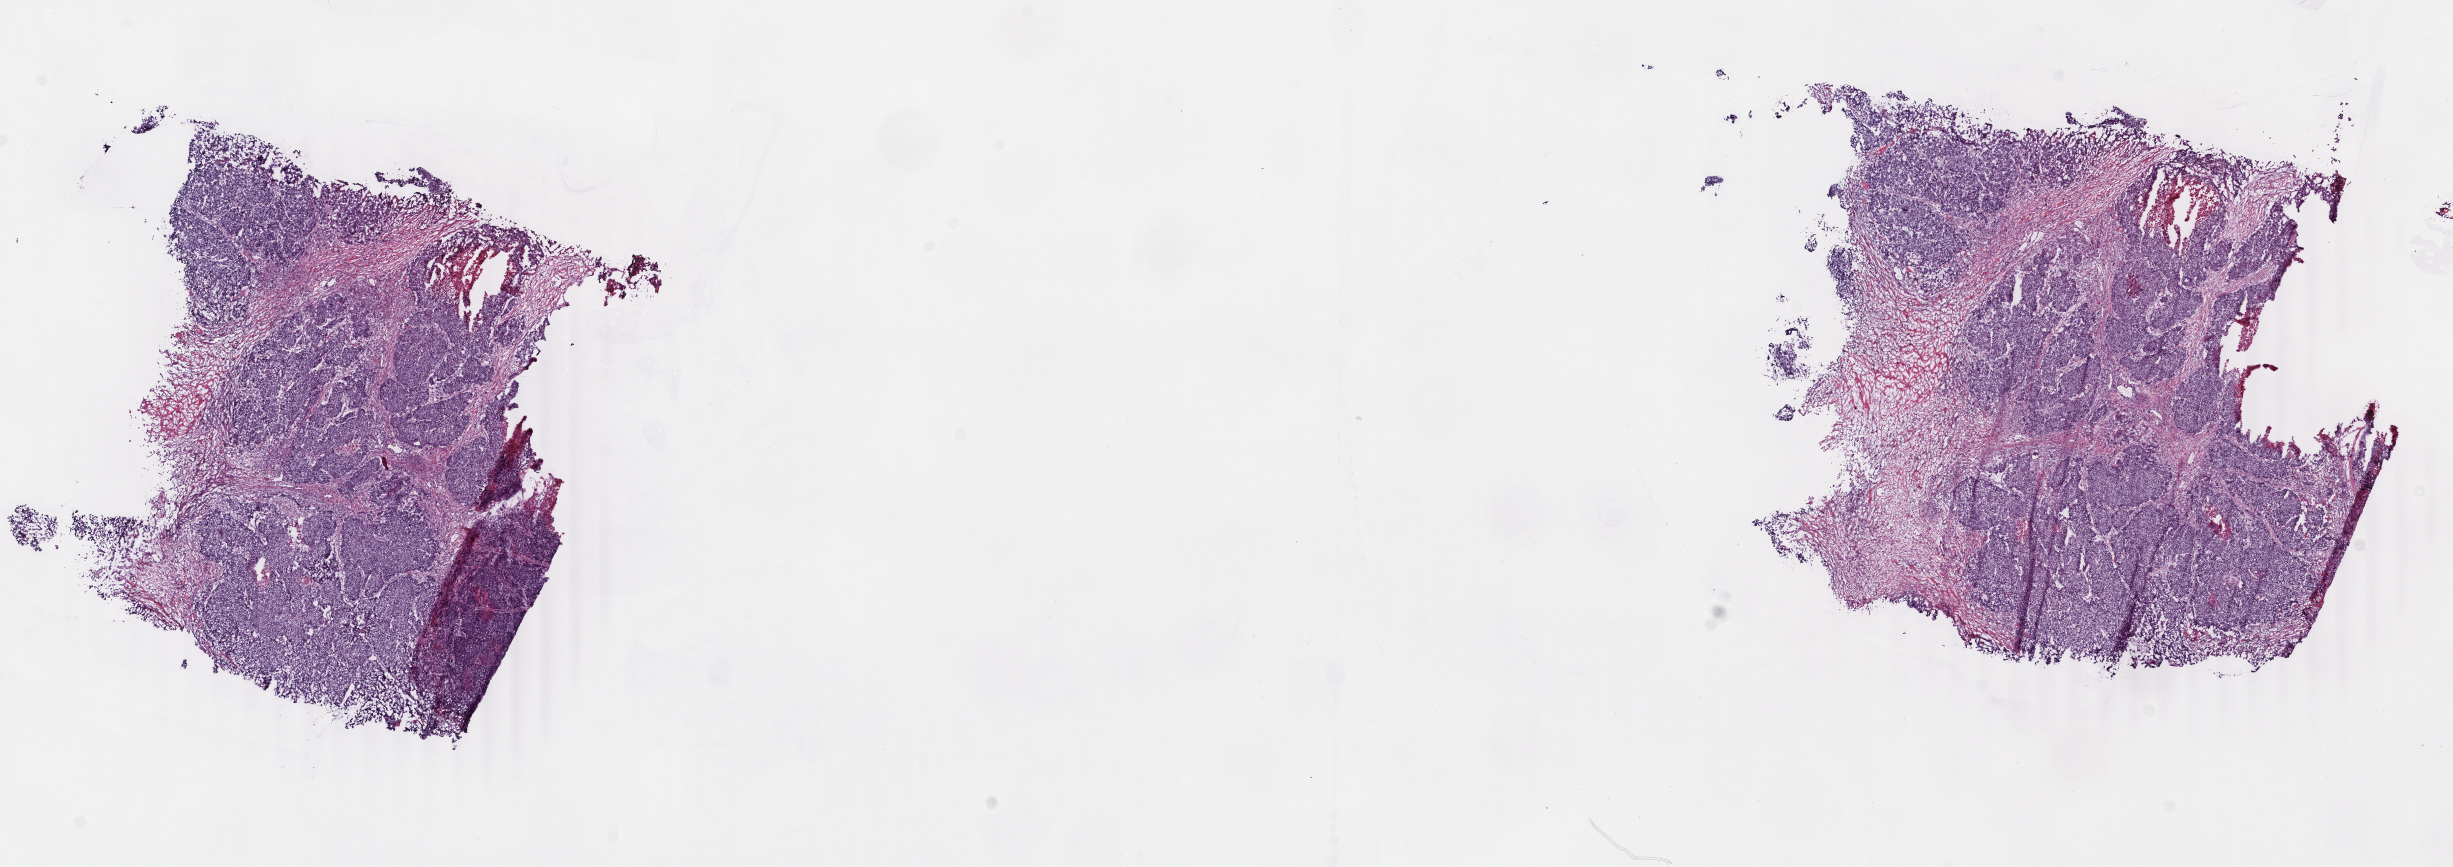
Digitized H&E tissue section (whole slide), whole scanned area (about 19.5 x 6.9 mm) shown as a low-resolution overview. Frozen section. Breast, primary tumour sample. Patient: female, age at initial diagnosis 69 years. Composition of this section per pathologist review: tumour cells 70%, tumour nuclei 85%.
Diagnosis: Infiltrating duct carcinoma, NOS.